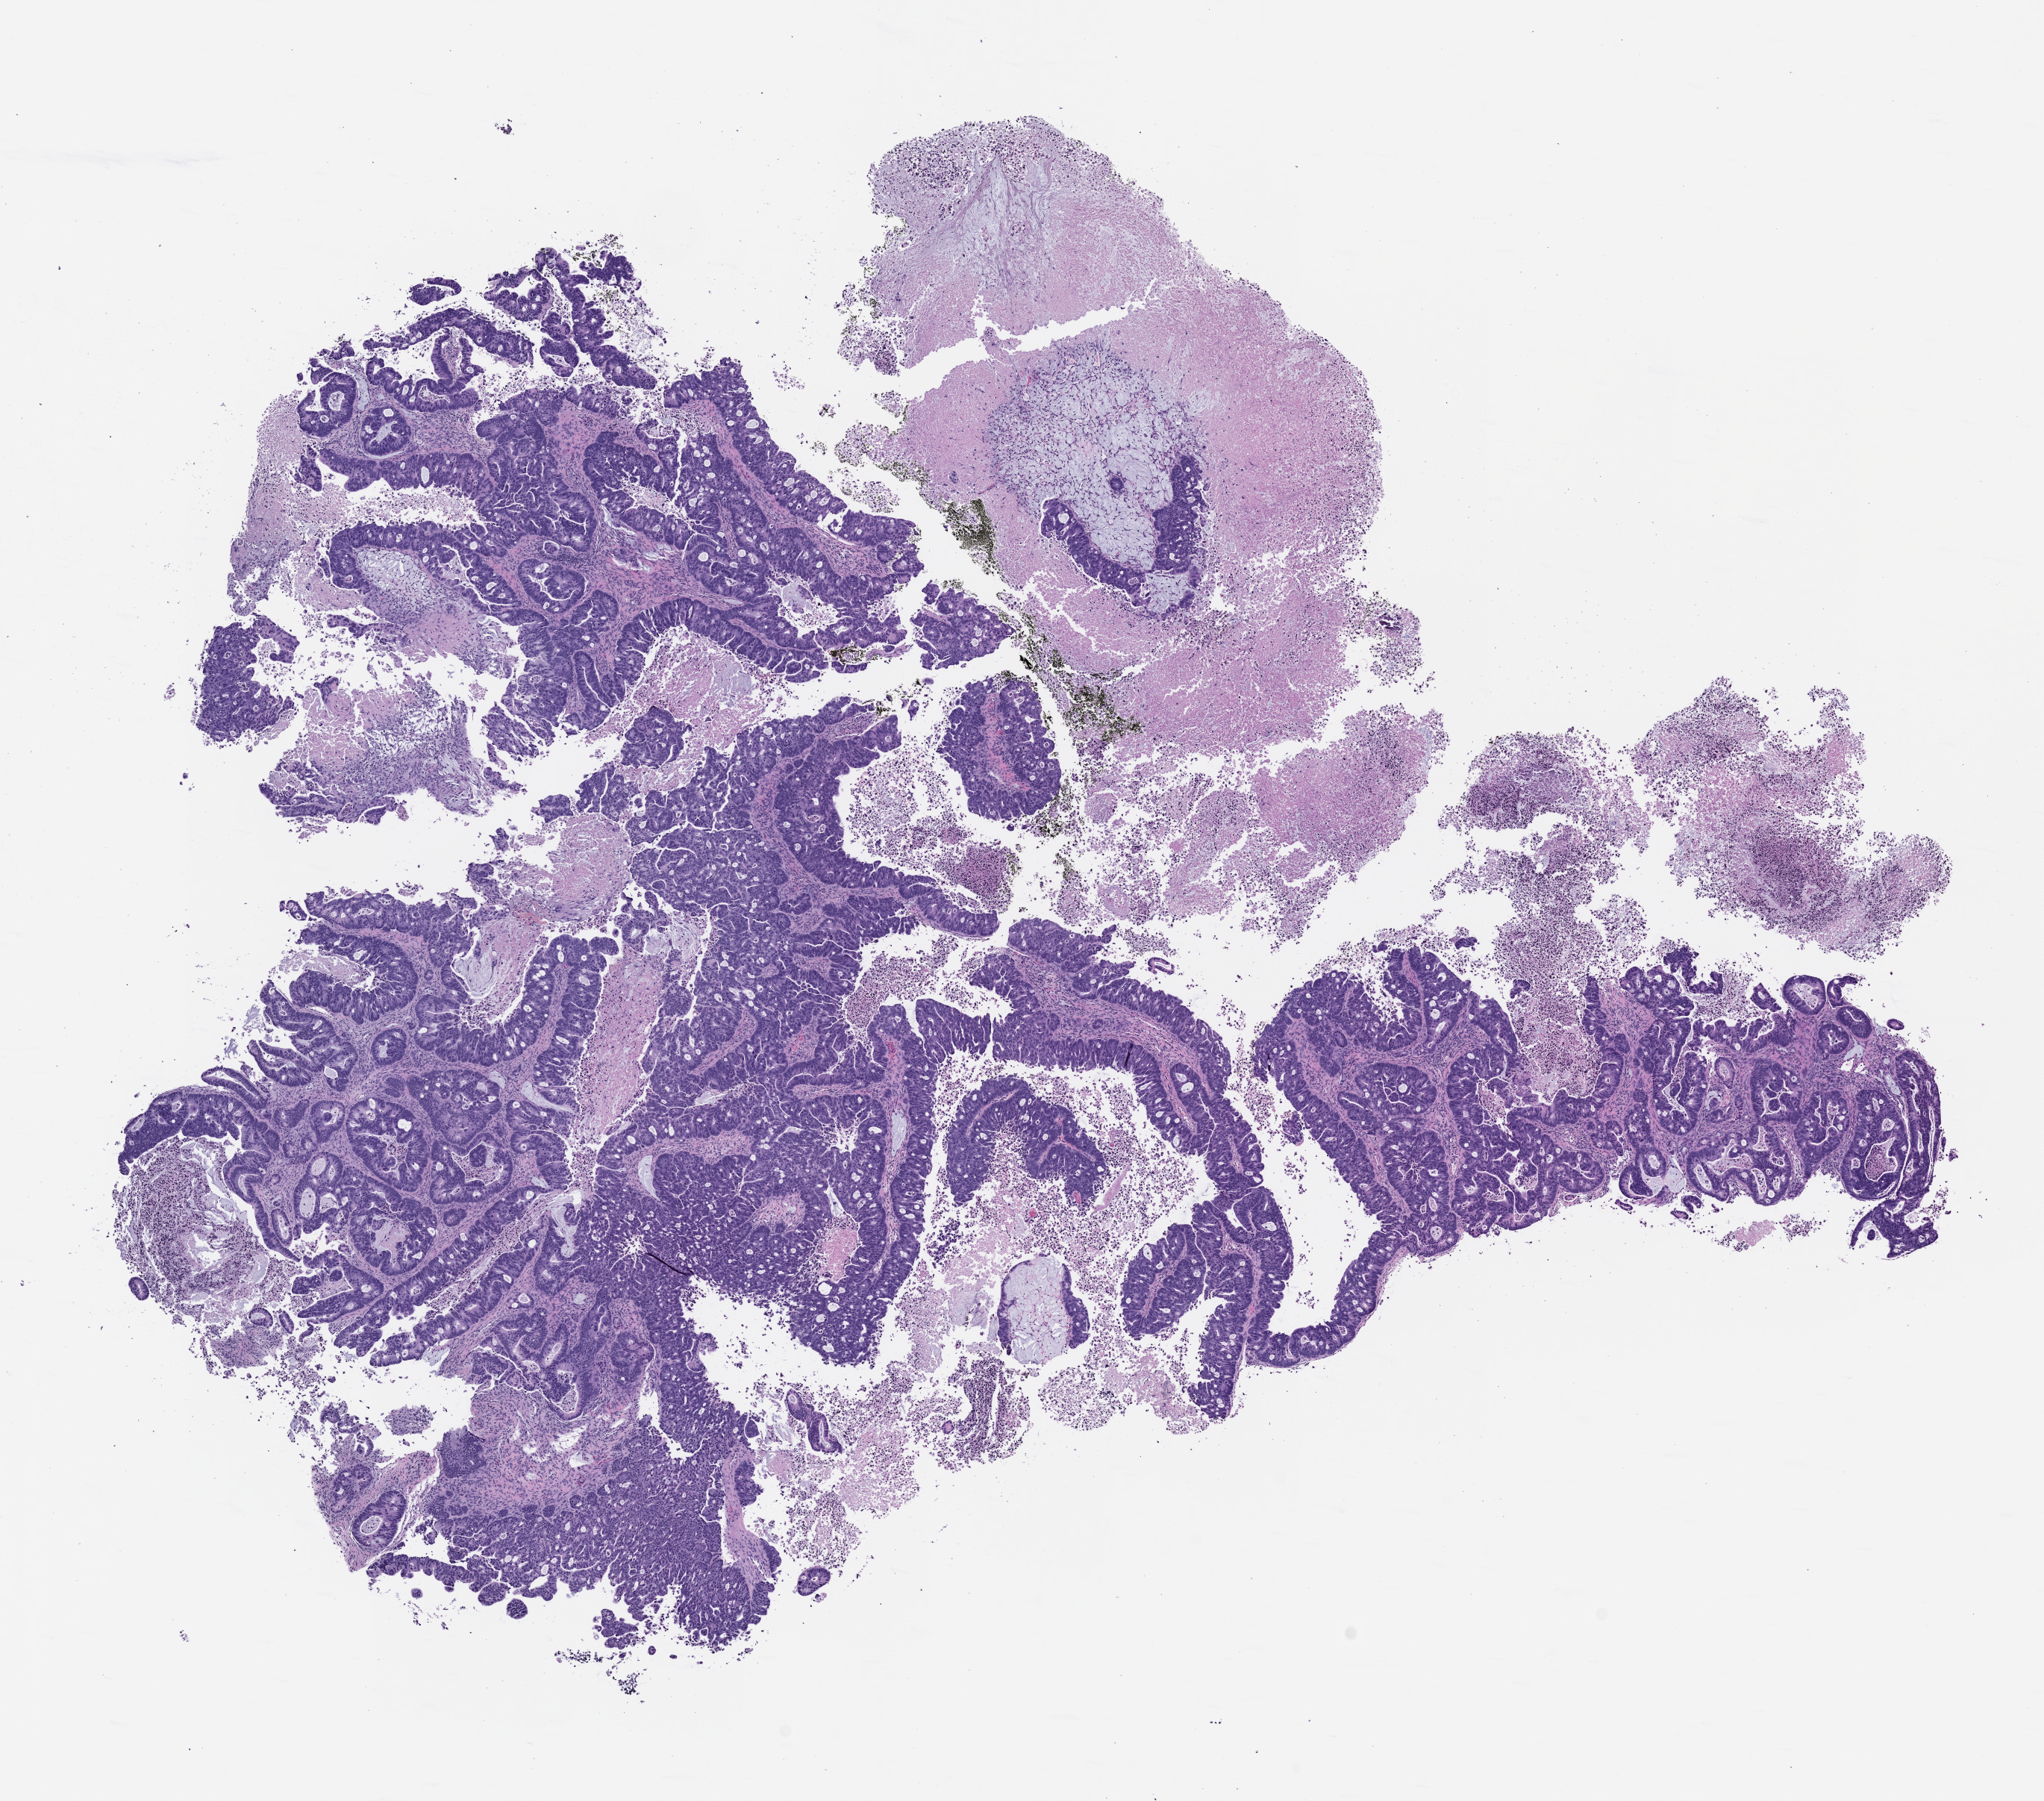
Haematoxylin and eosin whole-slide image of a patient-derived xenograft (PDX) tumor grown in a mouse, passage 1, shown as a low-resolution overview of the whole scanned area (about 11.0 x 9.7 mm); FFPE section; originating tumor site category: gastrointestinal tract.
* originating patient diagnosis: Colorectal Carcinoma